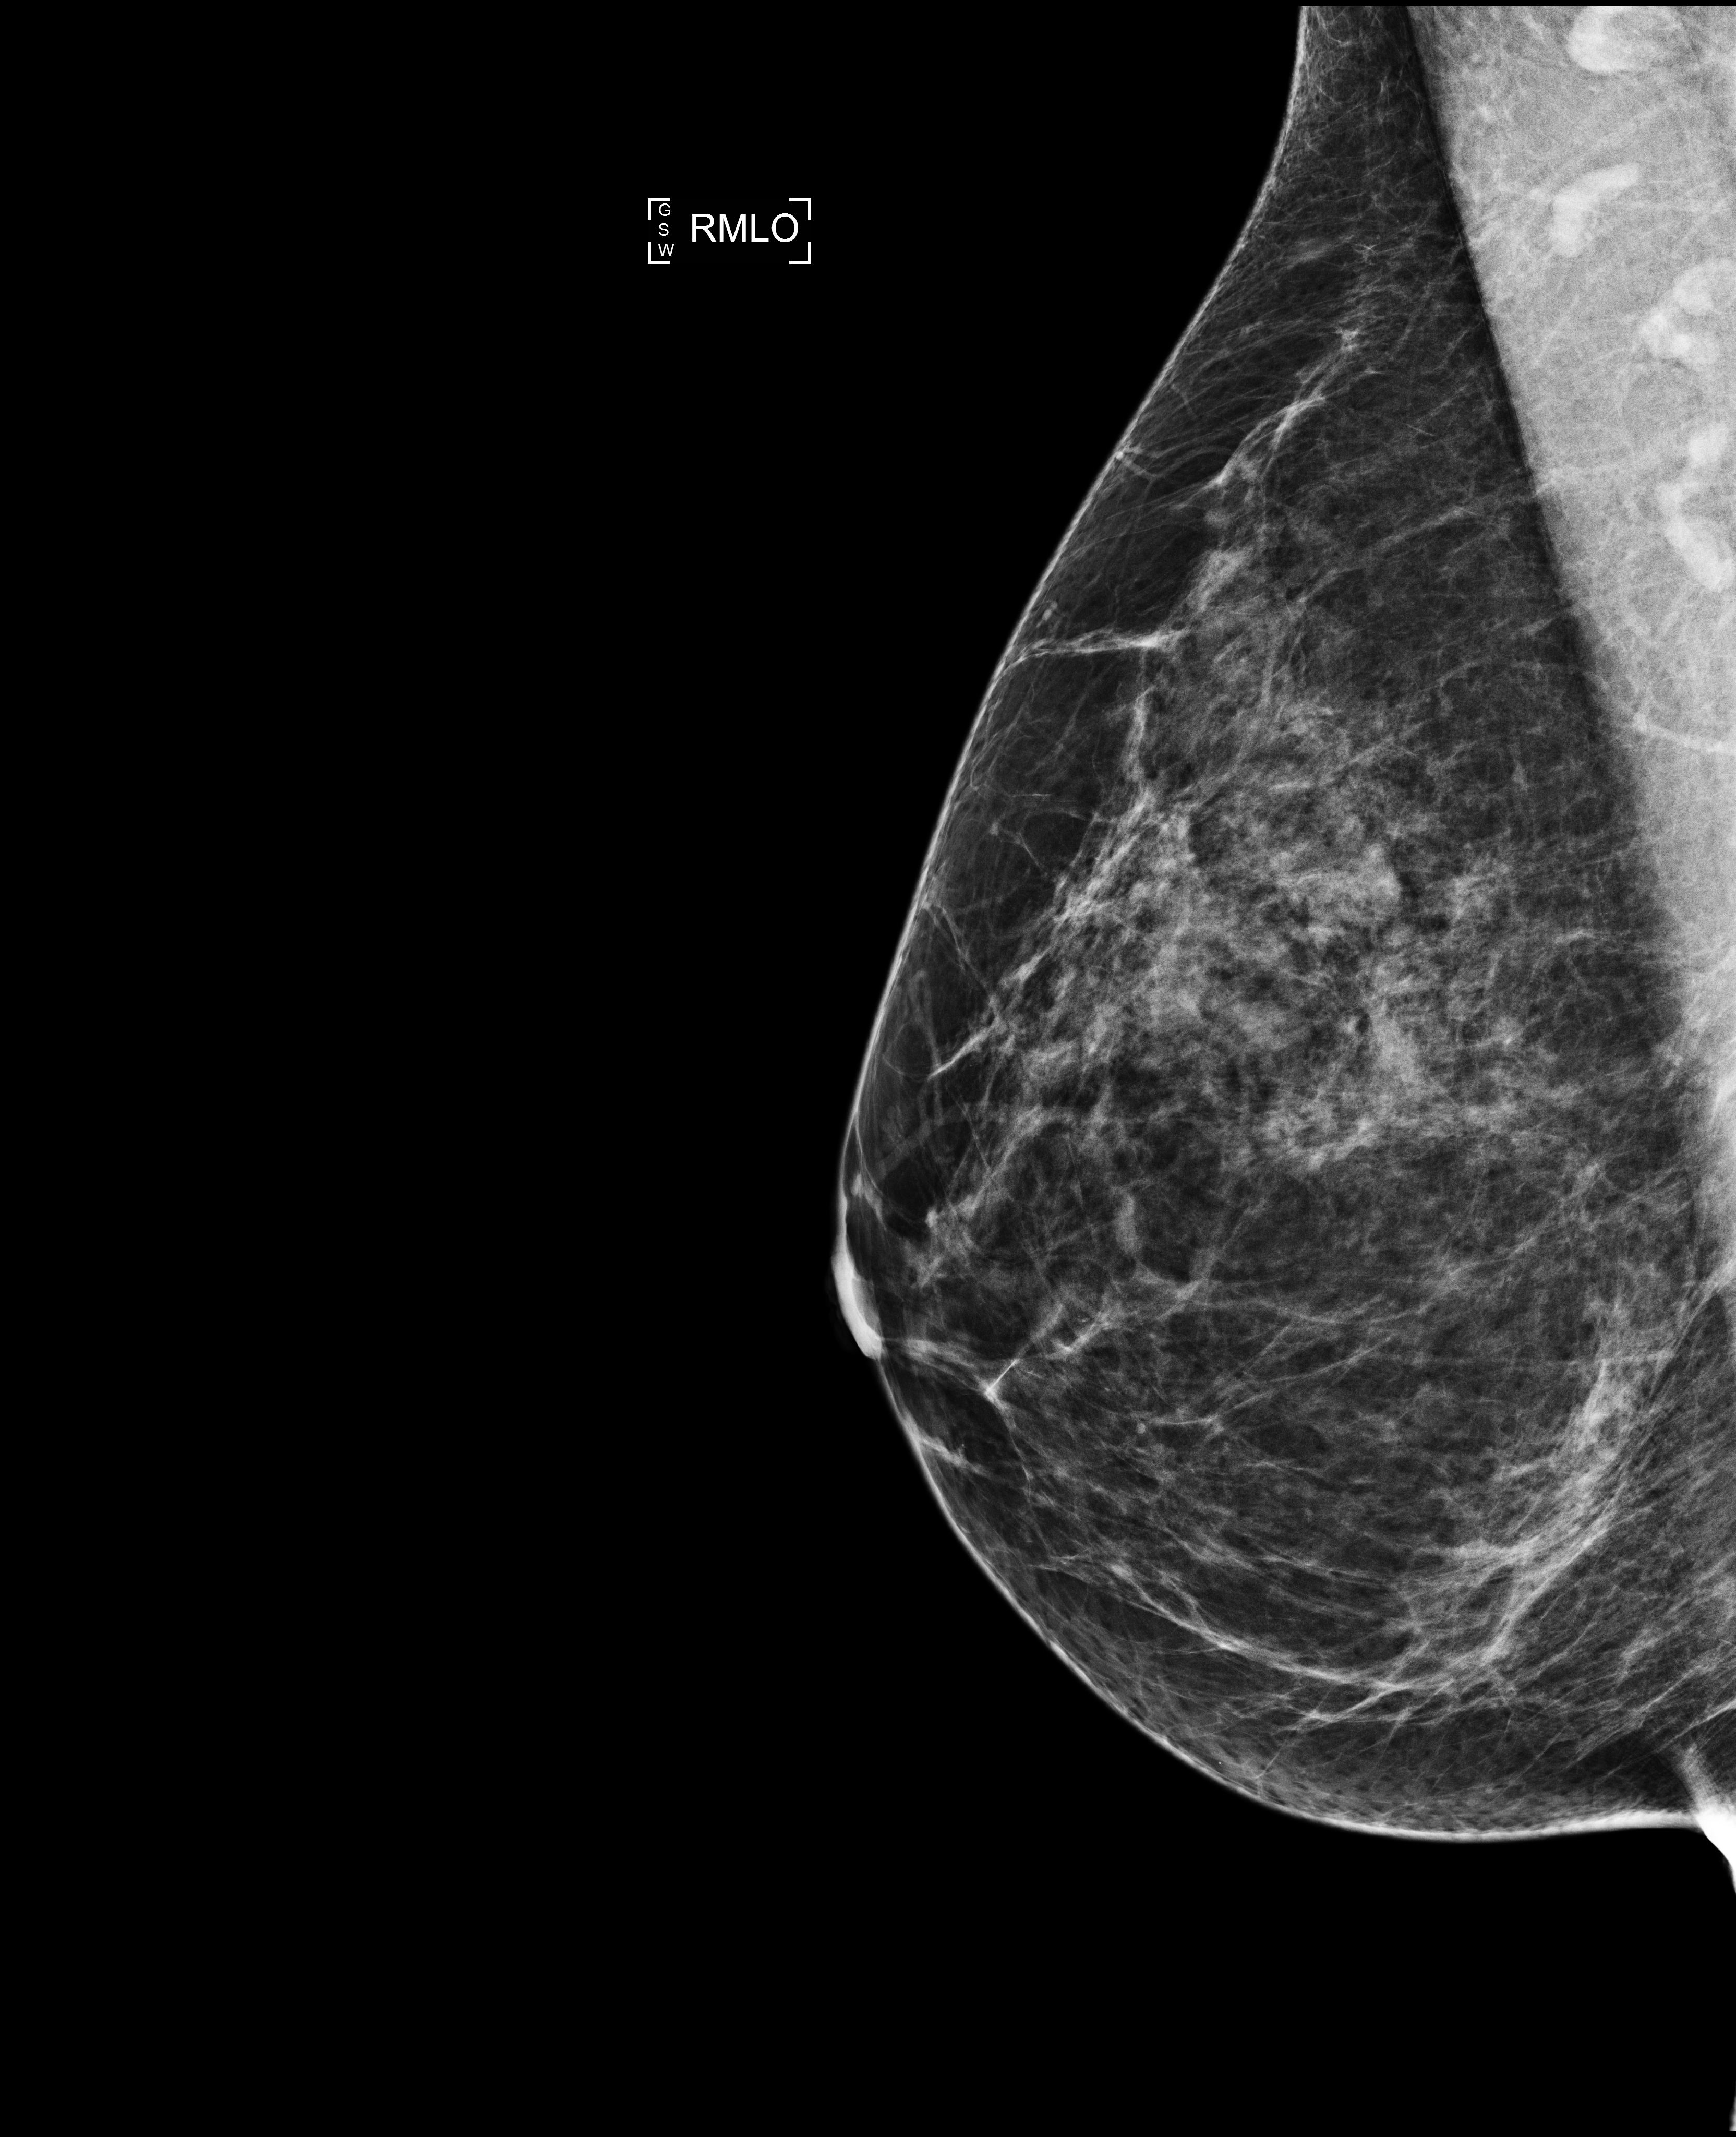
Digital mammogram (FFDM), right breast, MLO view, annual screening mammography examination, system: Selenia Dimensions. Female patient, age 51 years.
- BI-RADS breast density category at the screening exam (both breasts, scale 1–4): 3
- final BI-RADS category for the screening round (tomosynthesis exam, both breasts): category 1
- recall: no recall after this screen